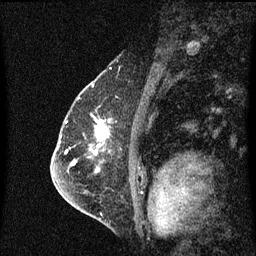
Breast MRI (dynamic contrast-enhanced), one sagittal slice. Position 42 of 60 along the scan axis. Dynamic contrast-enhanced series, image 2 of 3 at this slice position (ordered by acquisition). 1.5 T. TE 4.2 ms, TR 8.4 ms. 2 mm slice thickness. 256 × 256 image matrix, field of view 200 × 200 mm. Patient: female, 57 years. Case-level facts recorded for this patient, not image findings: setting: breast cancer imaged before/during neoadjuvant chemotherapy; receptor status: HR-positive, HER2-negative.
Structures marked on this image (semi-automatic segmentation, software-assisted and operator-edited):
- analysis volume of interest (the breast-tissue region the enhancement analysis was run in; not a lesion): bounding box (x1, y1, x2, y2) in pixels: (85, 122, 109, 145)
- tumour enhancement mask (voxels above the 70 % enhancement threshold inside the analysis volume of interest): (97, 122, 109, 141)